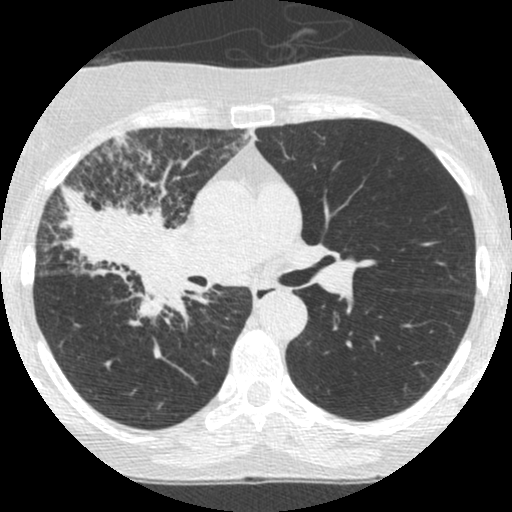
Low-dose screening chest CT, one axial slice. Slice 151 of 253 in the series (ordered by position). 120 kVp. Lung window (W 1500 / L -600 HU). 1.25 mm slice thickness. 512 × 512 image matrix.
Annotated regions visible in this slice (expert manual segmentation):
- lesion 2 (tumor, hilum of right lung): bounding box (x1, y1, x2, y2) in pixels: (49, 178, 184, 324)